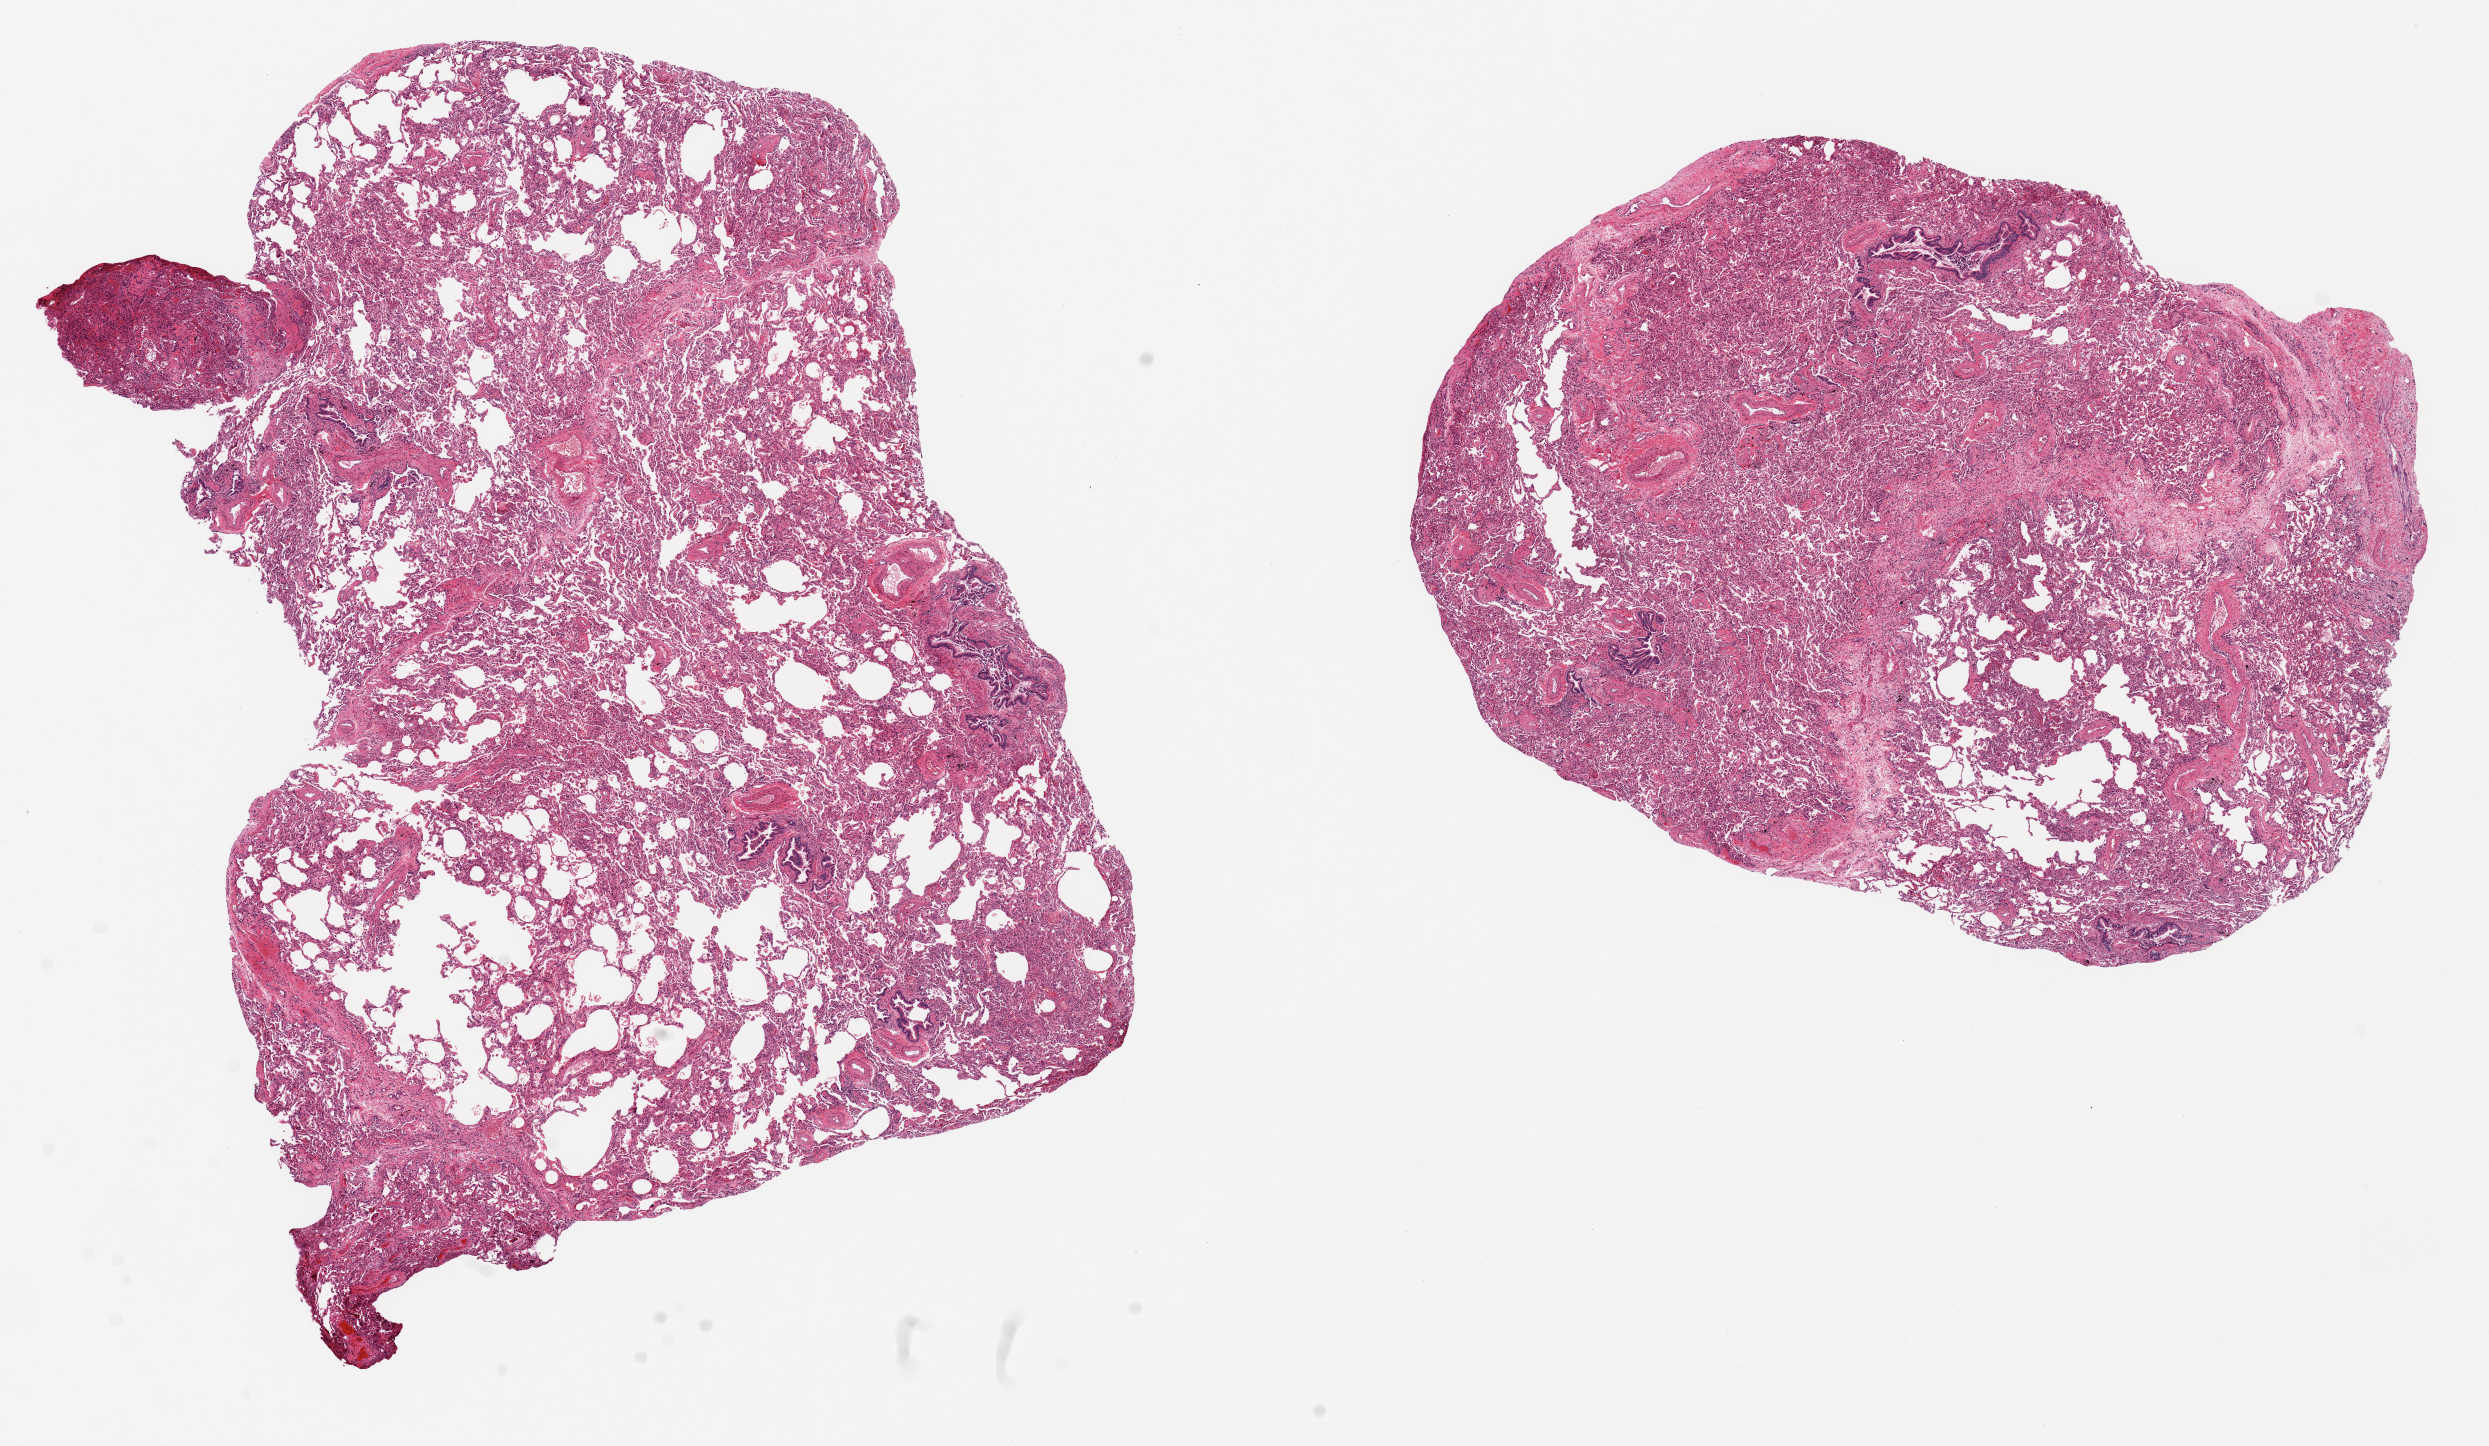
Hematoxylin and eosin (H&E) whole-slide image, a low-resolution overview of the entire scanned area, about 19.7 x 11.4 mm (acquisition: 20x scan), PAXgene-fixed, paraffin-embedded tissue, sampled site (target tissue): lung, tissue donor sample.
Review note (as recorded): 2 pieces, 7.5x5 & 10x7mm; Vascular sclerosis, focal emphysema and fibrosis; focus of aspiration pneumonia.